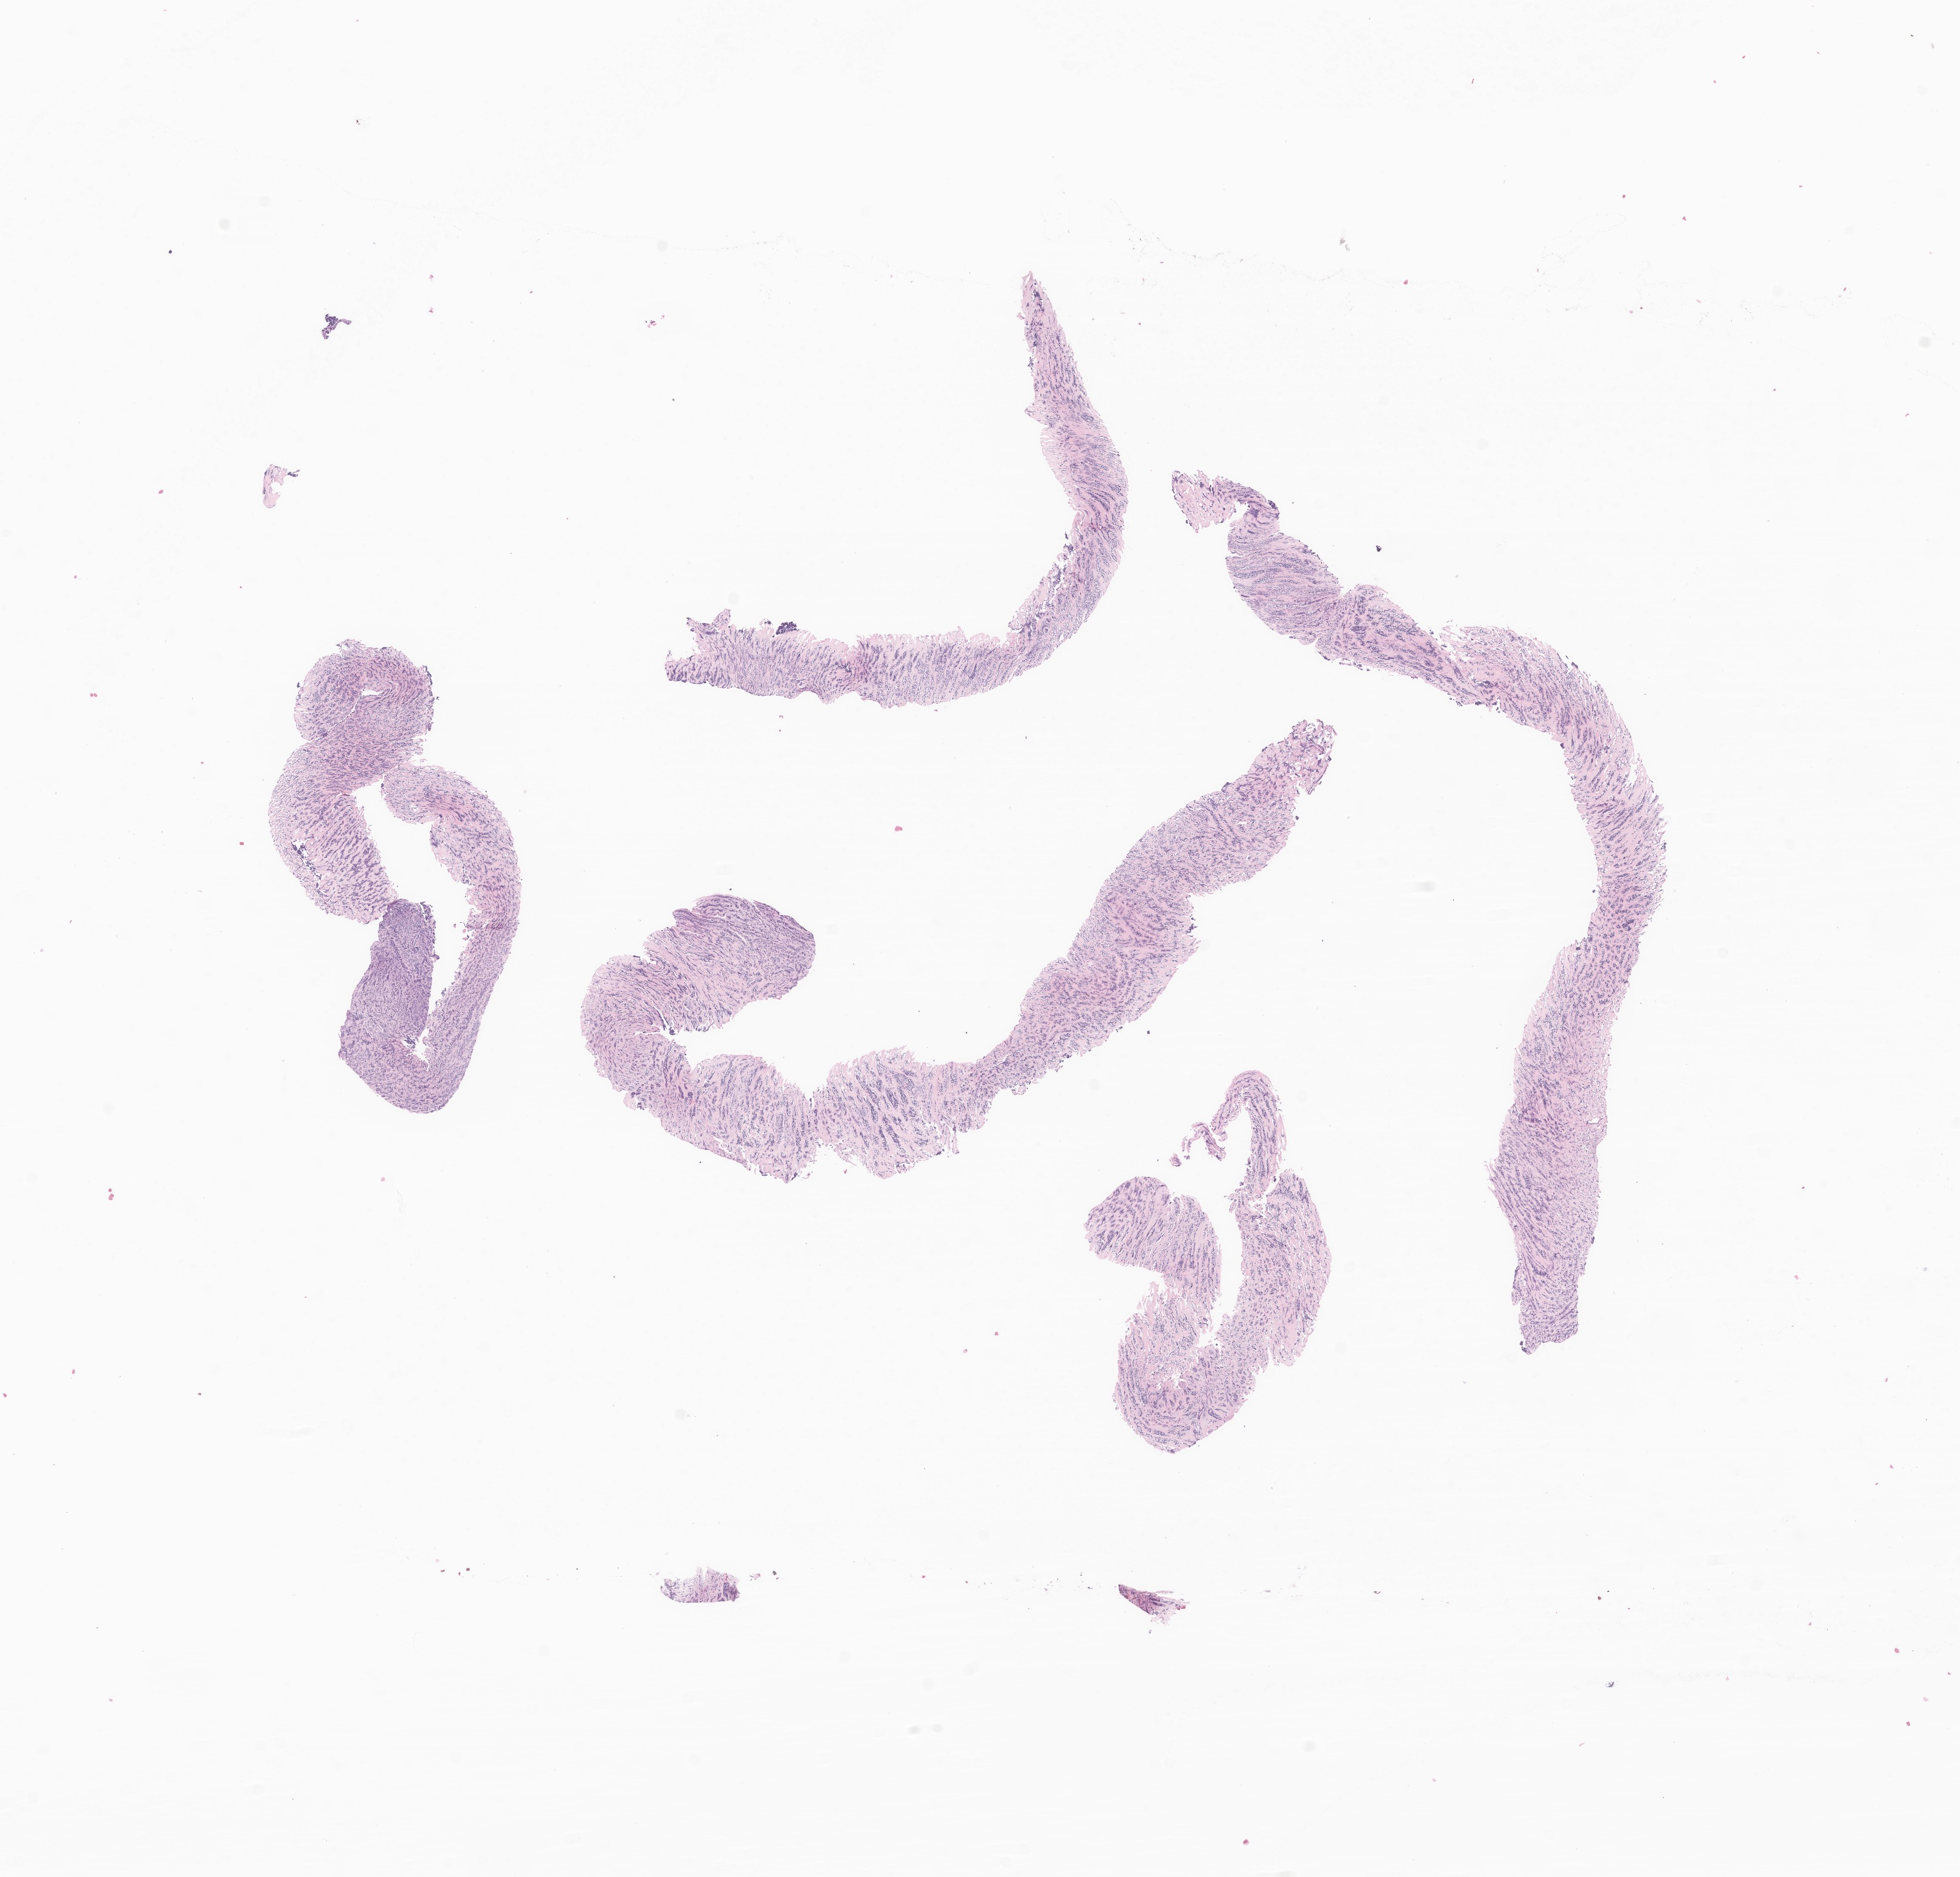
H&E whole-slide image of tumor tissue from the soft tissues of head and neck — a low-resolution overview of the entire scanned area, about 14.0 x 13.4 mm. FFPE section. Female patient, age 128 months (10 years 8 months).
Diagnosis (ICD-O-3 morphology term): Rhabdomyosarcoma, NOS.